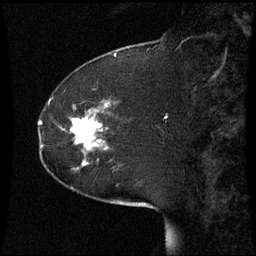
Breast MRI (dynamic contrast-enhanced), one sagittal slice; position 17 of 60 along the scan axis; dynamic contrast-enhanced series, image 2 of 3 at this slice position (ordered by acquisition); 1.5 T; TE 4.2 ms, TR 8.9 ms; 256 × 256 image matrix. Female patient, age 51 years. From the clinical record (not read from this slice): setting: breast cancer imaged before/during neoadjuvant chemotherapy; receptor status: HR-positive, HER2-negative.
Structures marked on this image (semi-automatically segmented with operator editing):
- analysis volume of interest (the breast-tissue region the enhancement analysis was run in; not a lesion): bounding box [x1, y1, x2, y2] px = [46, 102, 109, 169]
- tumour enhancement mask (voxels above the 70 % enhancement threshold inside the analysis volume of interest): [72, 118, 101, 145]